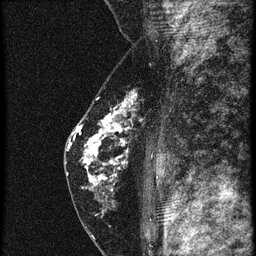
Breast MRI (dynamic contrast-enhanced), one sagittal slice; slice 35 of 60 in the series (ordered by position); 4 images stored at this slice position (order not interpretable as contrast timing); 1.5 T; TE 4.2 ms, TR 20.4 ms; 1.5 mm slice thickness; 256 × 256 image matrix, field of view 180 × 180 mm. Patient: female, 46 years. From the clinical record (not read from this slice): setting: breast cancer imaged before/during neoadjuvant chemotherapy; receptor status: triple-negative.
Annotated regions visible in this slice (semi-automatic segmentation, software-assisted and operator-edited):
- analysis volume of interest (the breast-tissue region the enhancement analysis was run in; not a lesion): bounding box <67,88,153,201> (left, top, right, bottom; pixels)
- tumour enhancement mask (voxels above the 90 % enhancement threshold inside the analysis volume of interest): <69,98,135,195>